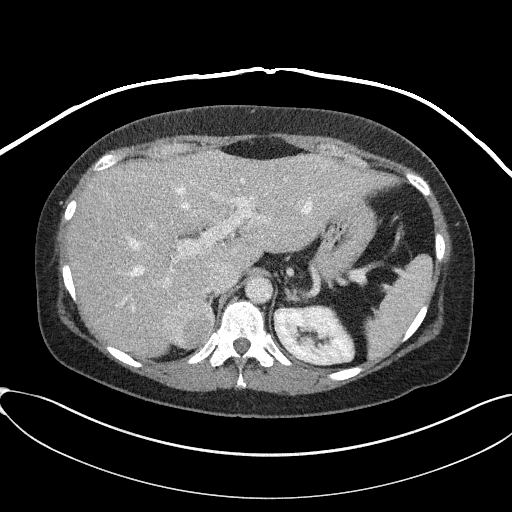
Contrast-enhanced abdominal CT, one axial slice. Position 61 of 95 along the scan axis. Reconstruction kernel I41f/2. 100 kVp. Intravenous contrast given. Soft-tissue window (W 400 / L 40 HU). 512 × 512 image matrix, field of view 410 × 410 mm. Patient: female, 46 years. From the clinical record (not read from this slice): diagnosis: adrenocortical carcinoma; tumour side: right adrenal; tumour size at pathology: 7.2 cm; Ki-67 index: 50 %; stage (as recorded): 4.
Annotated regions visible in this slice (semi-automatic segmentation, software-assisted and operator-edited):
- mass: box from (x=165, y=296) to (x=213, y=347) px